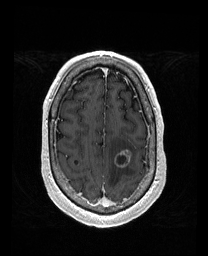
Brain MRI from a brain-tumour surgery series, one axial slice; position 141 of 192 along the scan axis; T1-weighted post-contrast; 1 mm slice thickness; 208 × 256 image matrix, field of view 211 × 260 mm. Case-level facts recorded for this patient, not image findings: histopathology: Metastatic Carcinoma from Lung Adenocarcinoma; tumour location: Left Frontal.
Structures marked on this image (expert manual segmentation):
- tumour: bounding box [x1, y1, x2, y2] px = [114, 151, 131, 167]